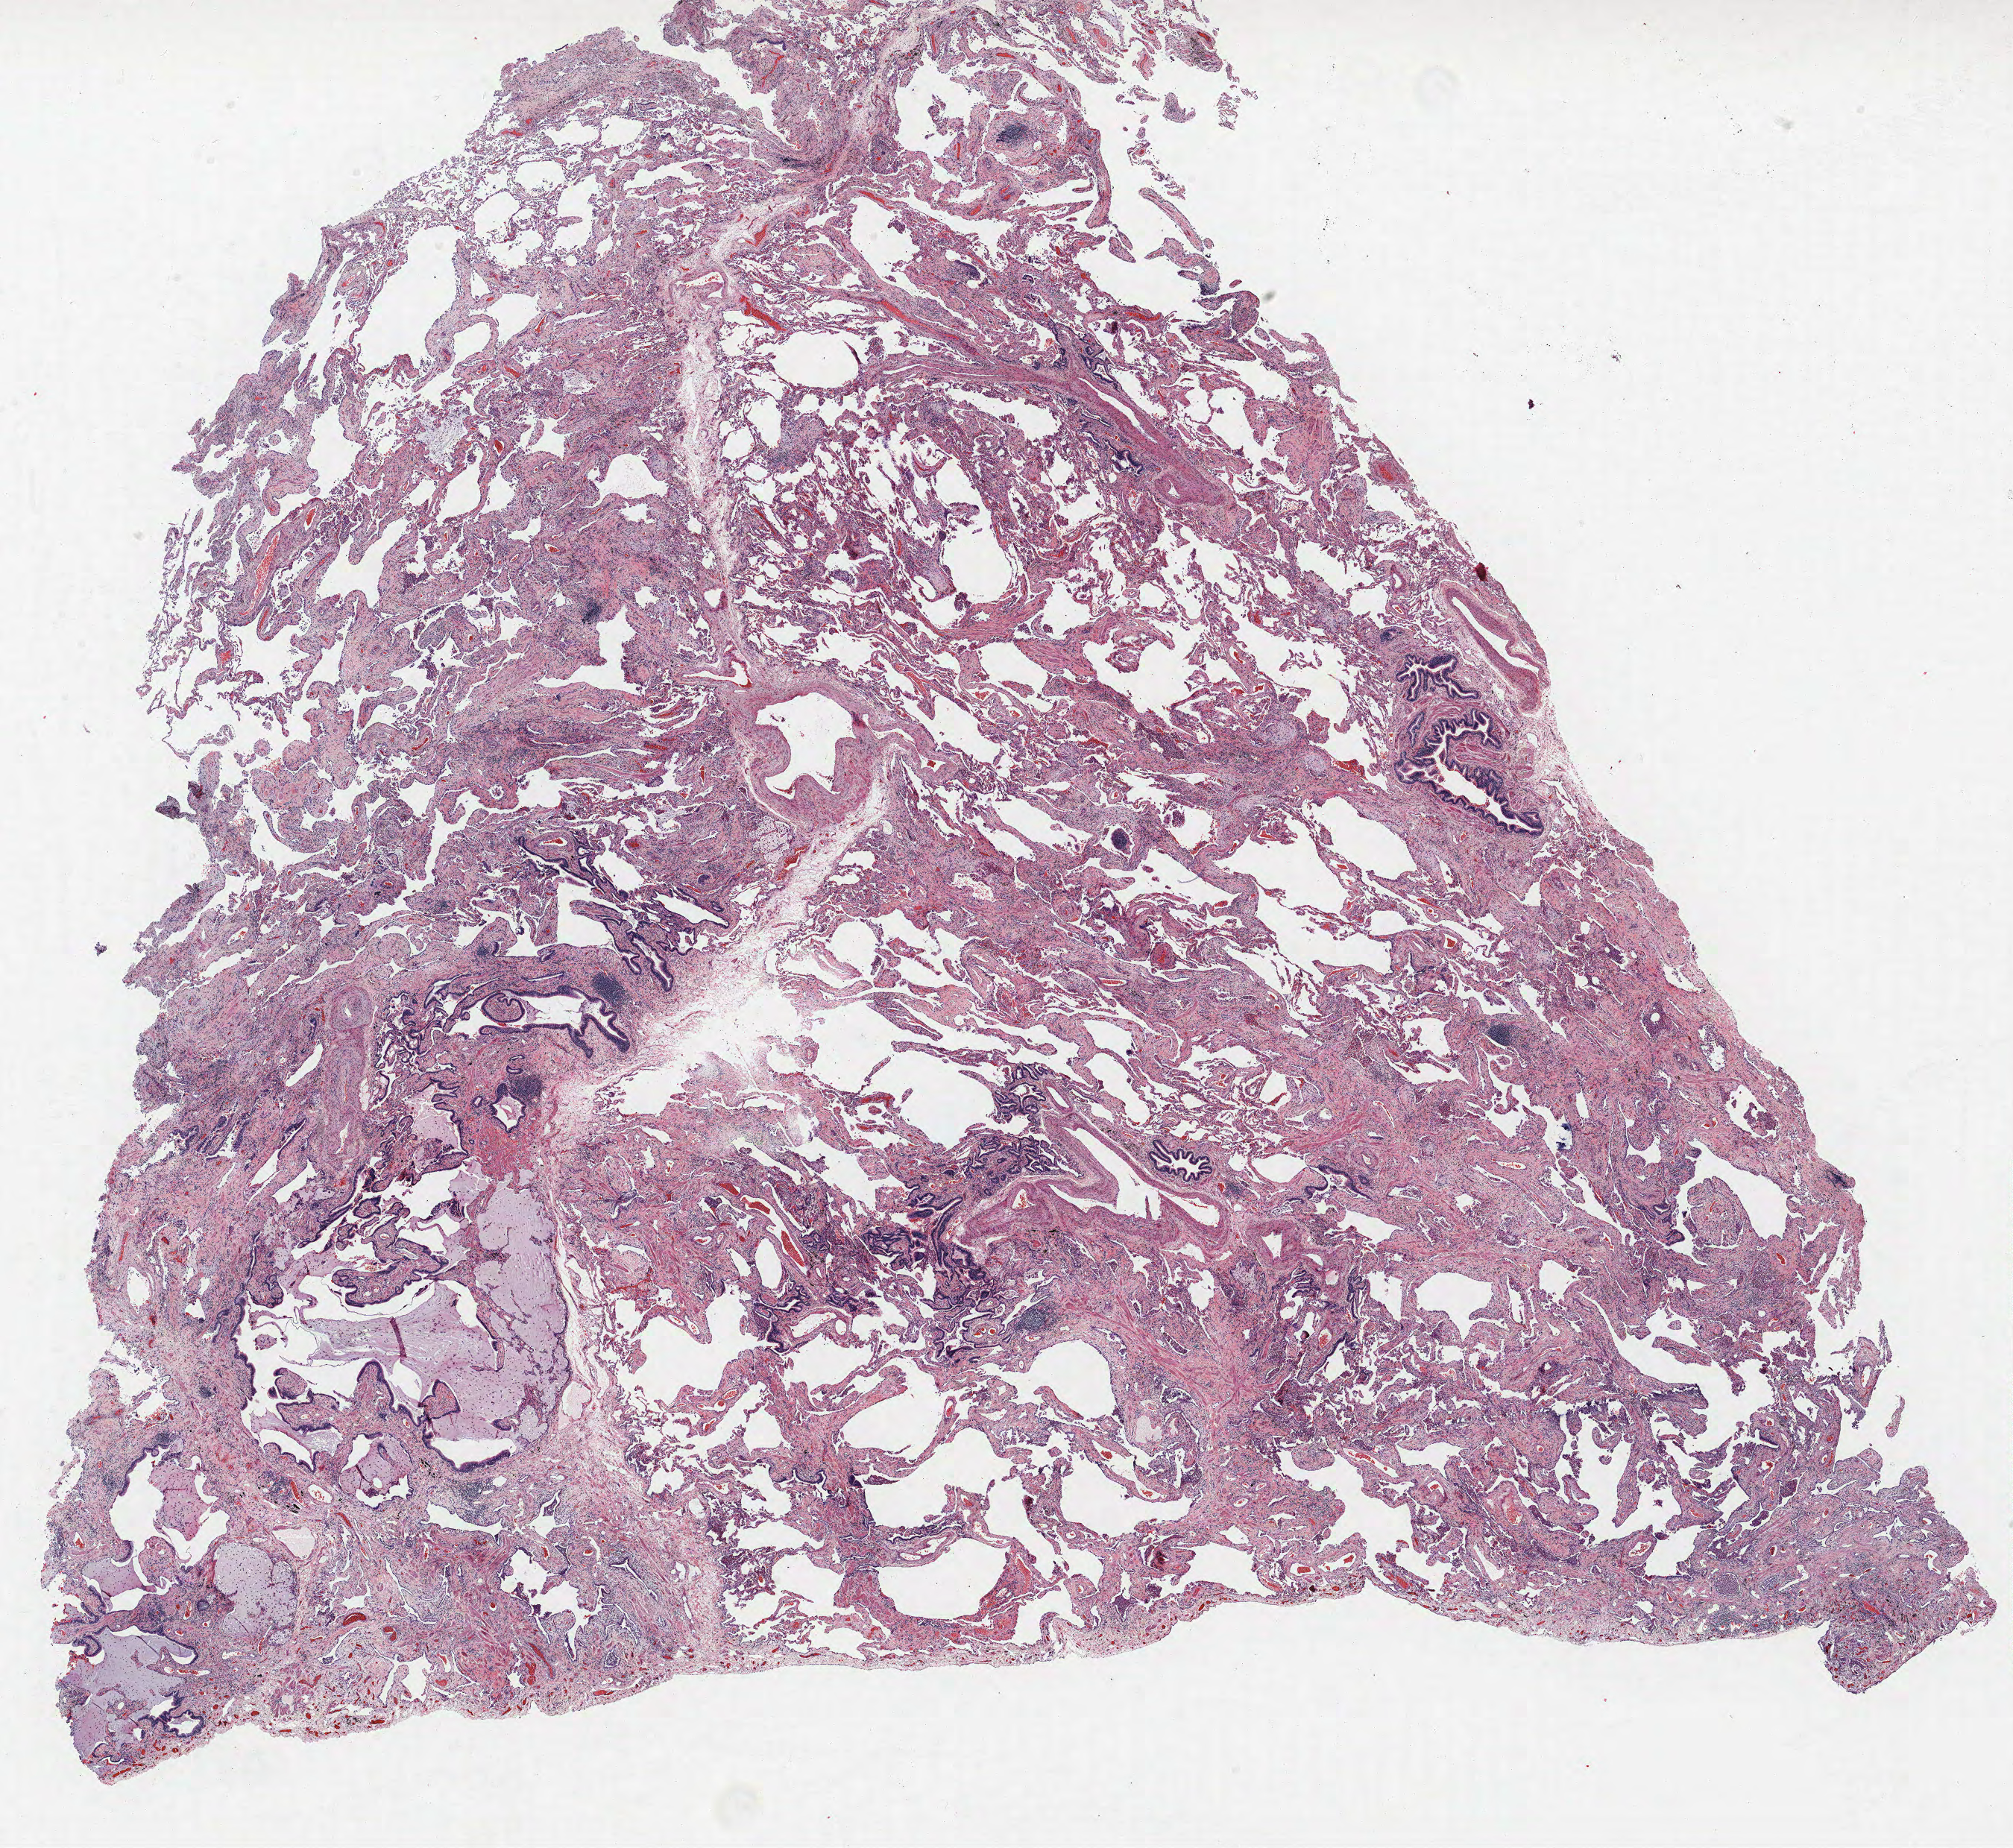
H&E-stained whole-slide image, whole scanned area (about 21.6 x 19.8 mm) shown as a low-resolution overview. Formalin-fixed paraffin-embedded (FFPE) section. Lung. Female patient, aged 56 at enrolment. Current smoker at enrolment. Grade: moderately differentiated (G2).
• participant's lung-cancer diagnosis: Squamous cell carcinoma, NOS
• primary tumour location (clinical record): right lower lobe
• tumour size (pathology): 17 mm
• stage (AJCC 6th edition): IA